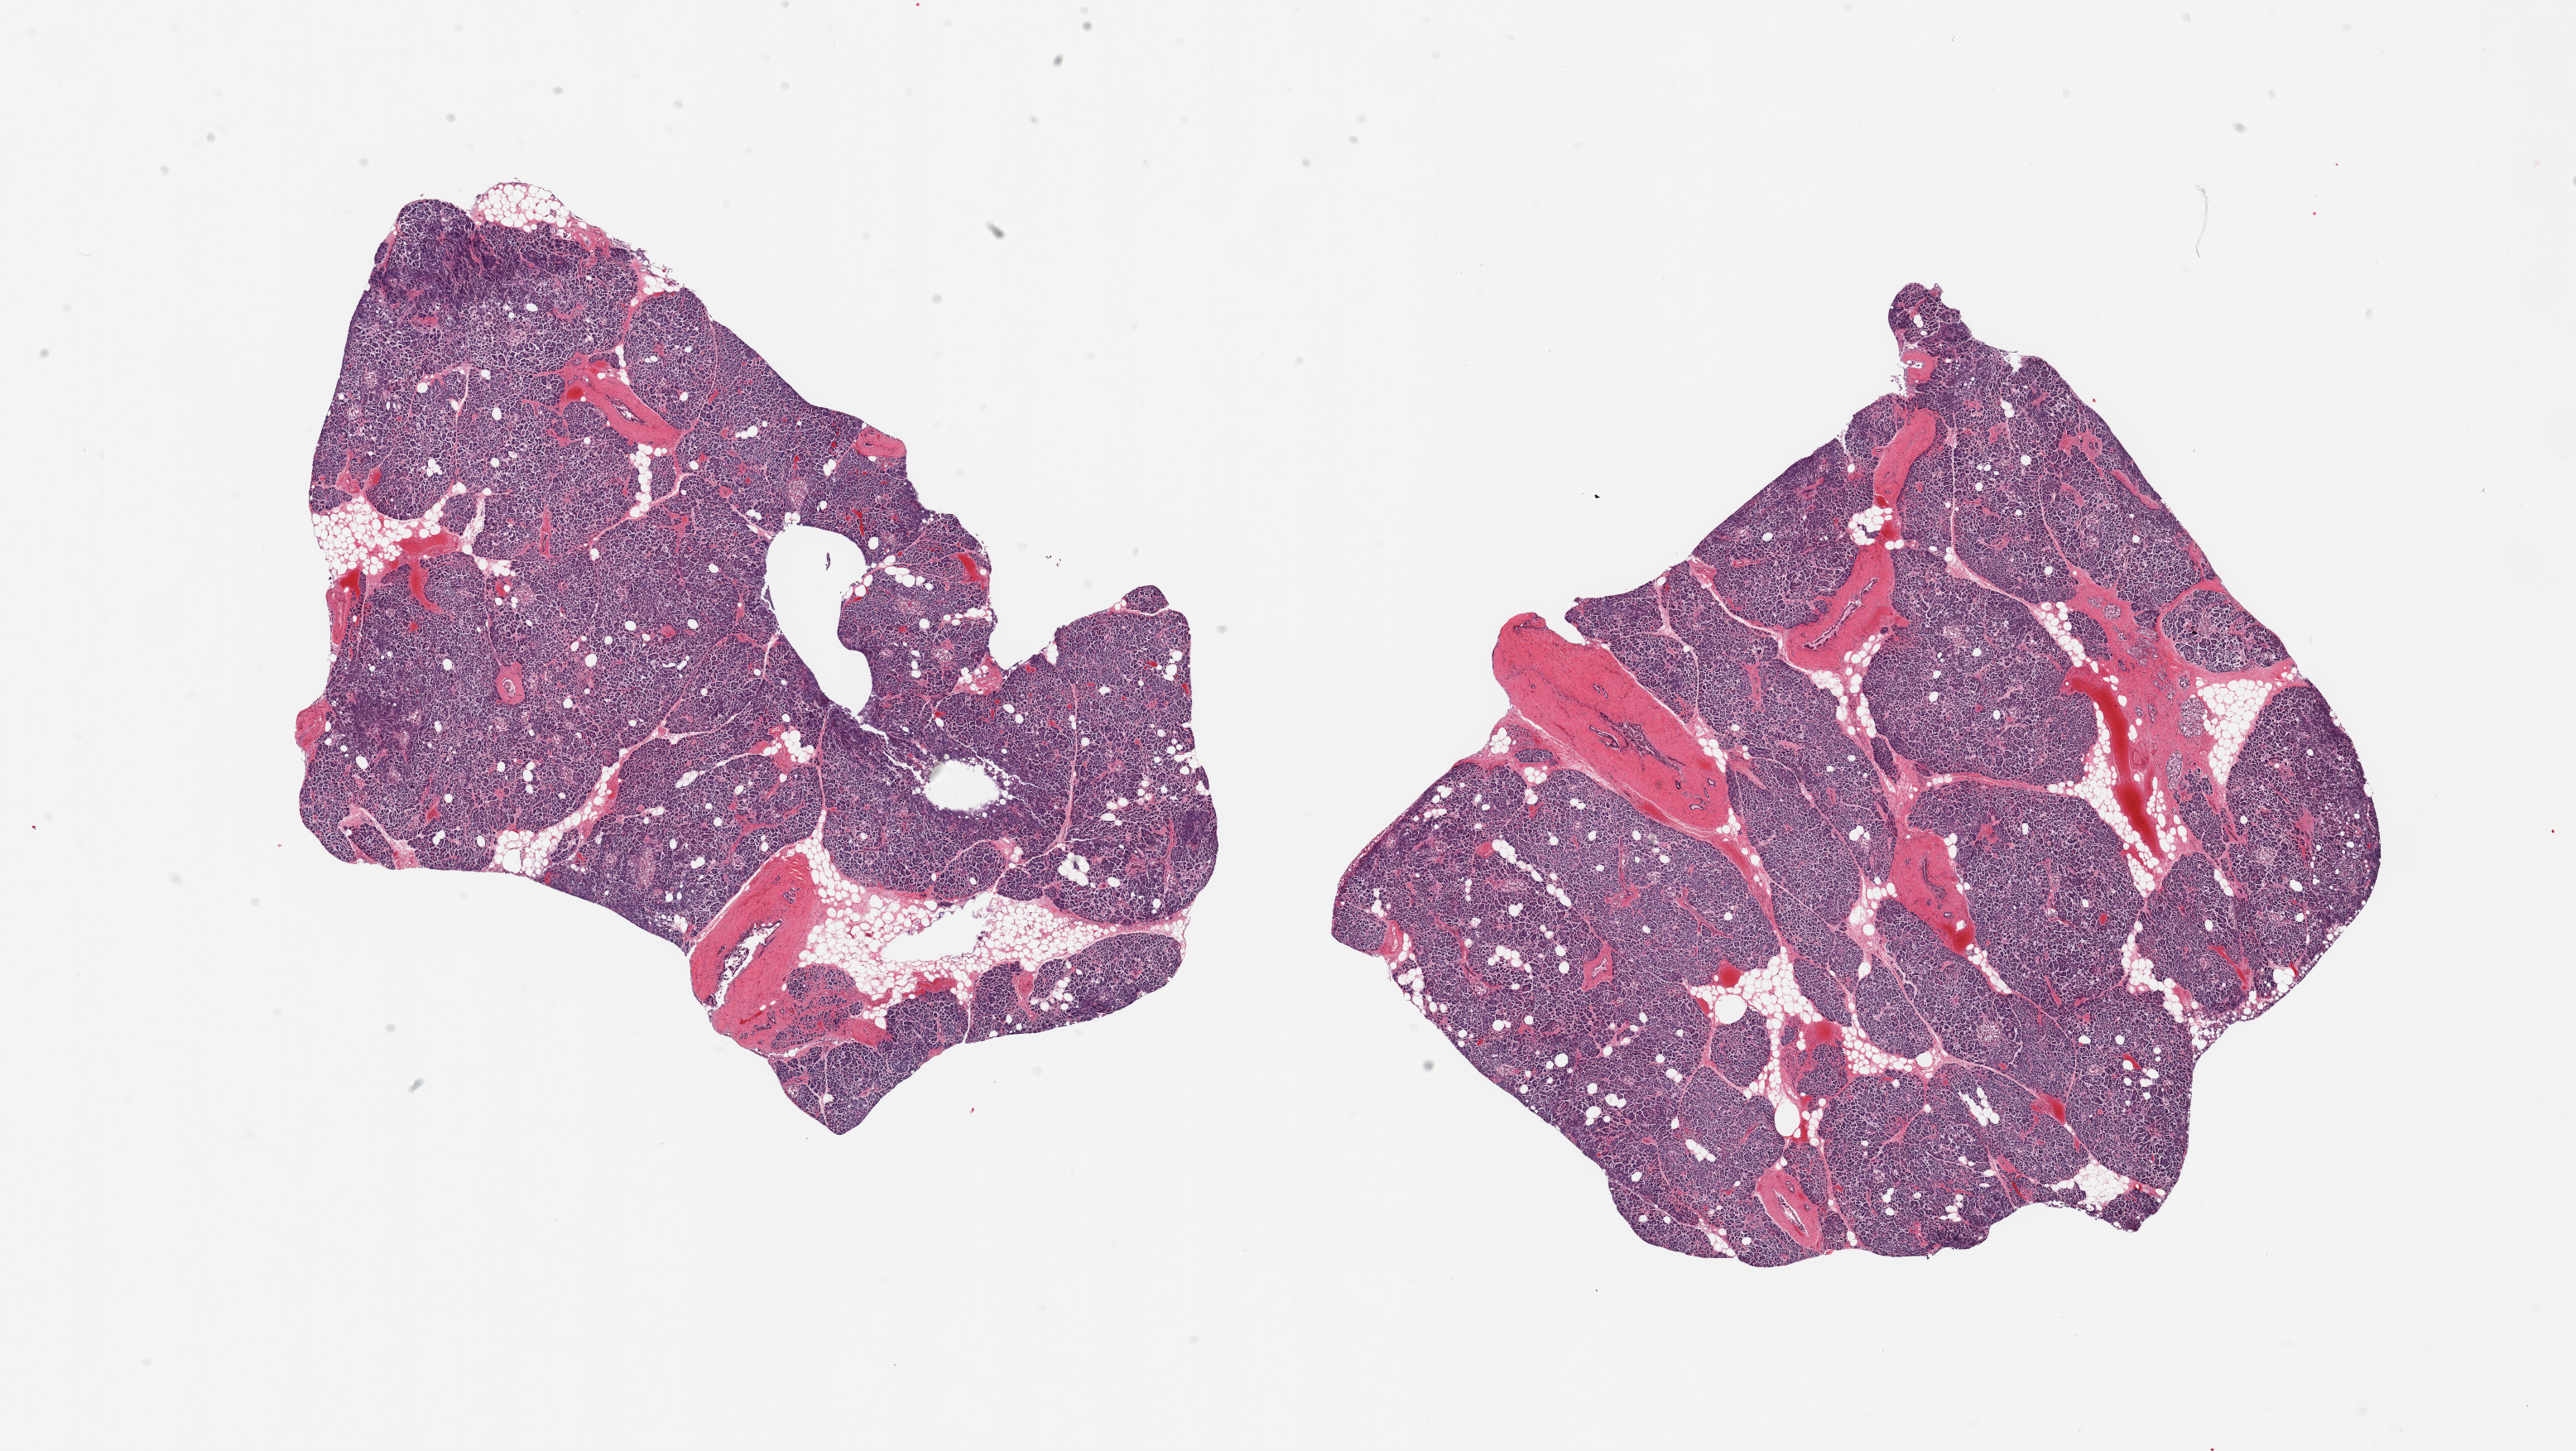
Whole-slide image, haematoxylin and eosin stain, shown as a low-resolution overview of the whole scanned area (about 24.6 x 13.9 mm, slide scanned at 20x). PAXgene-fixed, paraffin-embedded tissue. Sampled site (target tissue): pancreas. Donor tissue sample.
Reviewer comment on this tissue sample: 2 pieces, moderately advanced saponification; Islets still visible, moderately-severely degraded.